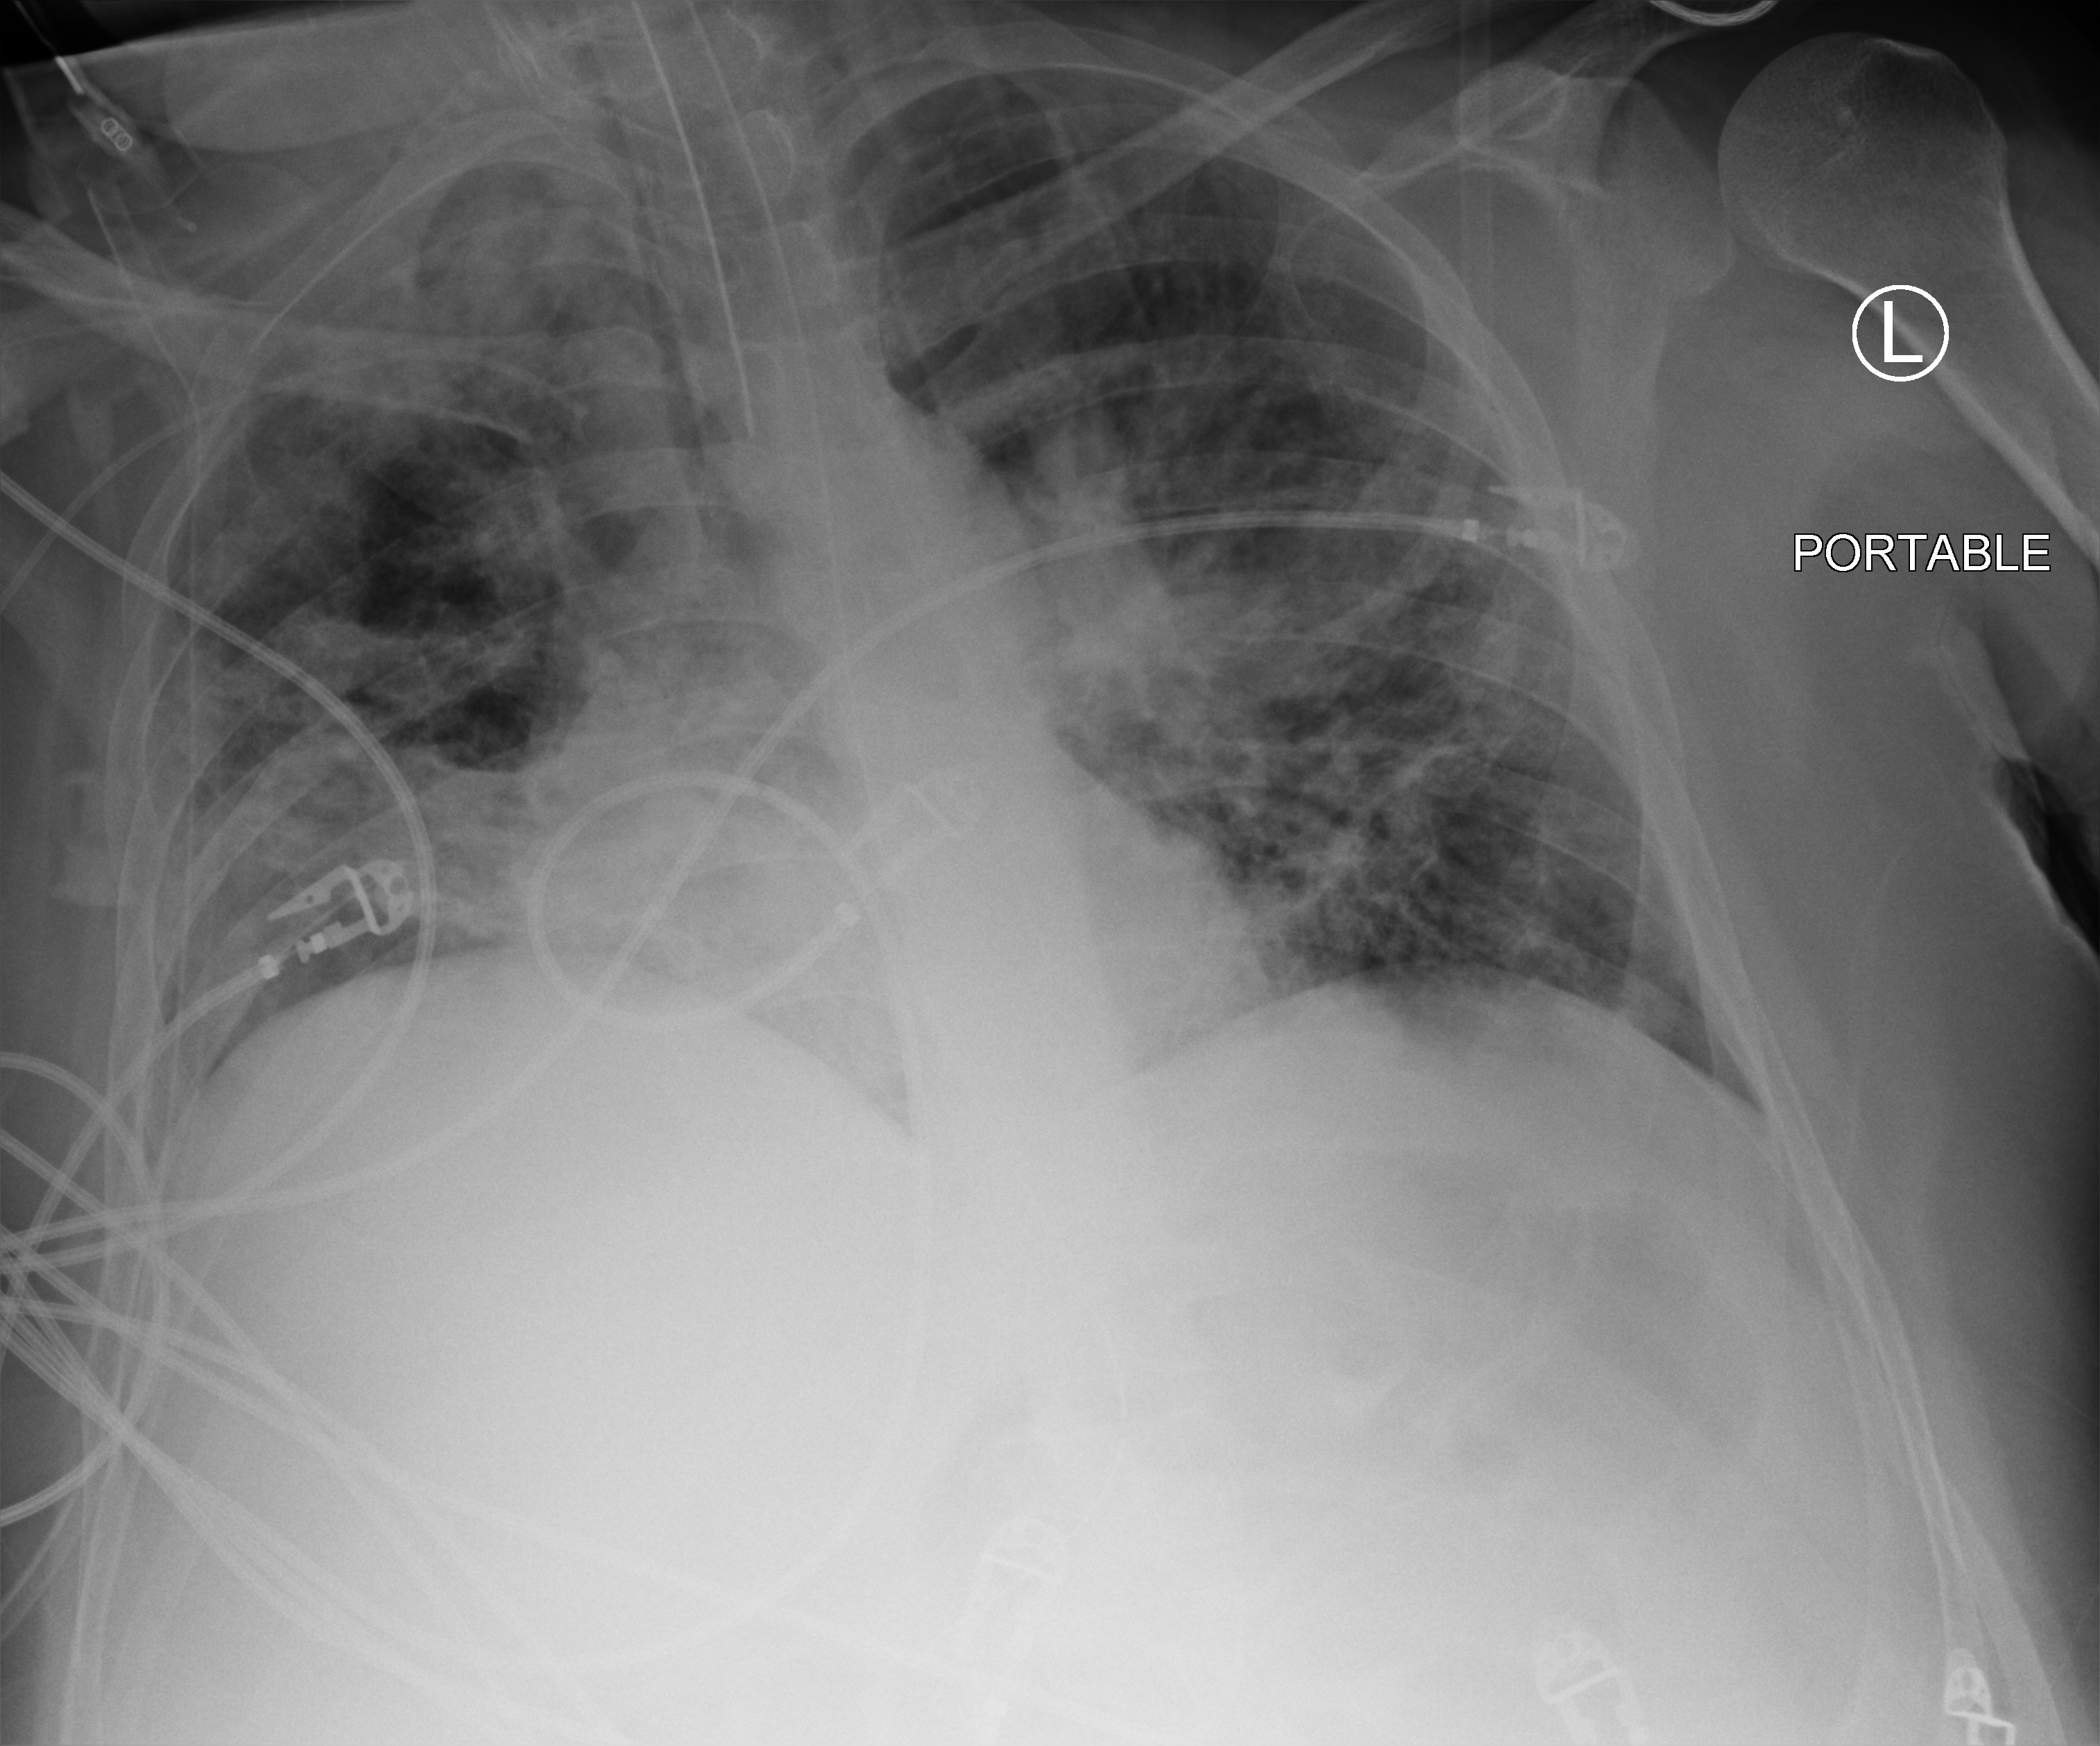
Bedside chest radiograph (computed radiography). Adult patient hospitalised with COVID-19, age 18–59 years.
Admission-level facts for this patient (not findings on this image; timing relative to this image not recorded):
- mechanically ventilated during this hospital stay: yes
- admitted to intensive care during this hospital stay: yes